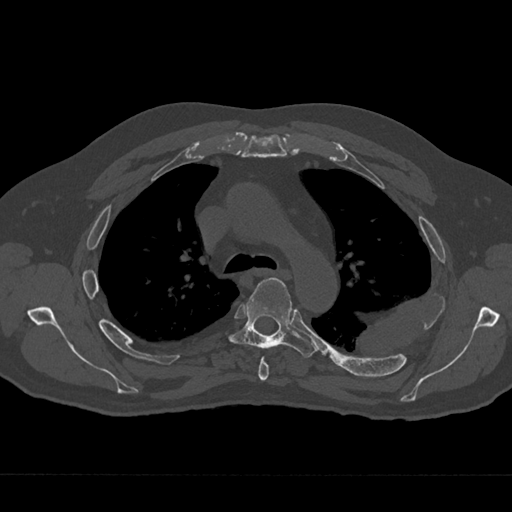
CT including the spine, one axial slice. 120 kVp. Bone window (W 1800 / L 400 HU). 0.5 mm slice thickness. 512 × 512 image matrix, field of view 377 × 377 mm. Male patient, age 75 years. Case-level facts recorded for this patient, not image findings: primary cancer: renal; vertebrae with lytic lesions (as recorded): T4.
Annotated regions visible in this slice (semi-automatic segmentation, software-assisted and operator-edited):
- T4 vertebra: bounding box <258,356,269,381> (left, top, right, bottom; pixels)
- T5 vertebra: <226,278,317,358>